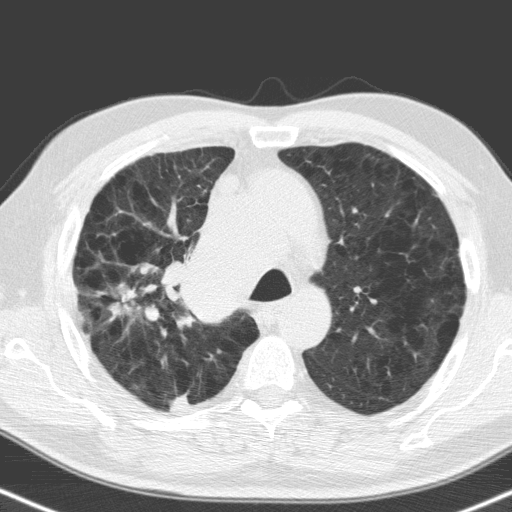
Low-dose screening chest CT, one axial slice. Slice 118 of 160 in the series (ordered by position). Lung window (W 1500 / L -600 HU). 512 × 512 image matrix.
Structures marked on this image (manually delineated by an expert):
- lesion 1 (tumor, hilum of right lung): bounding box (x1, y1, x2, y2) in pixels: (166, 226, 242, 322)